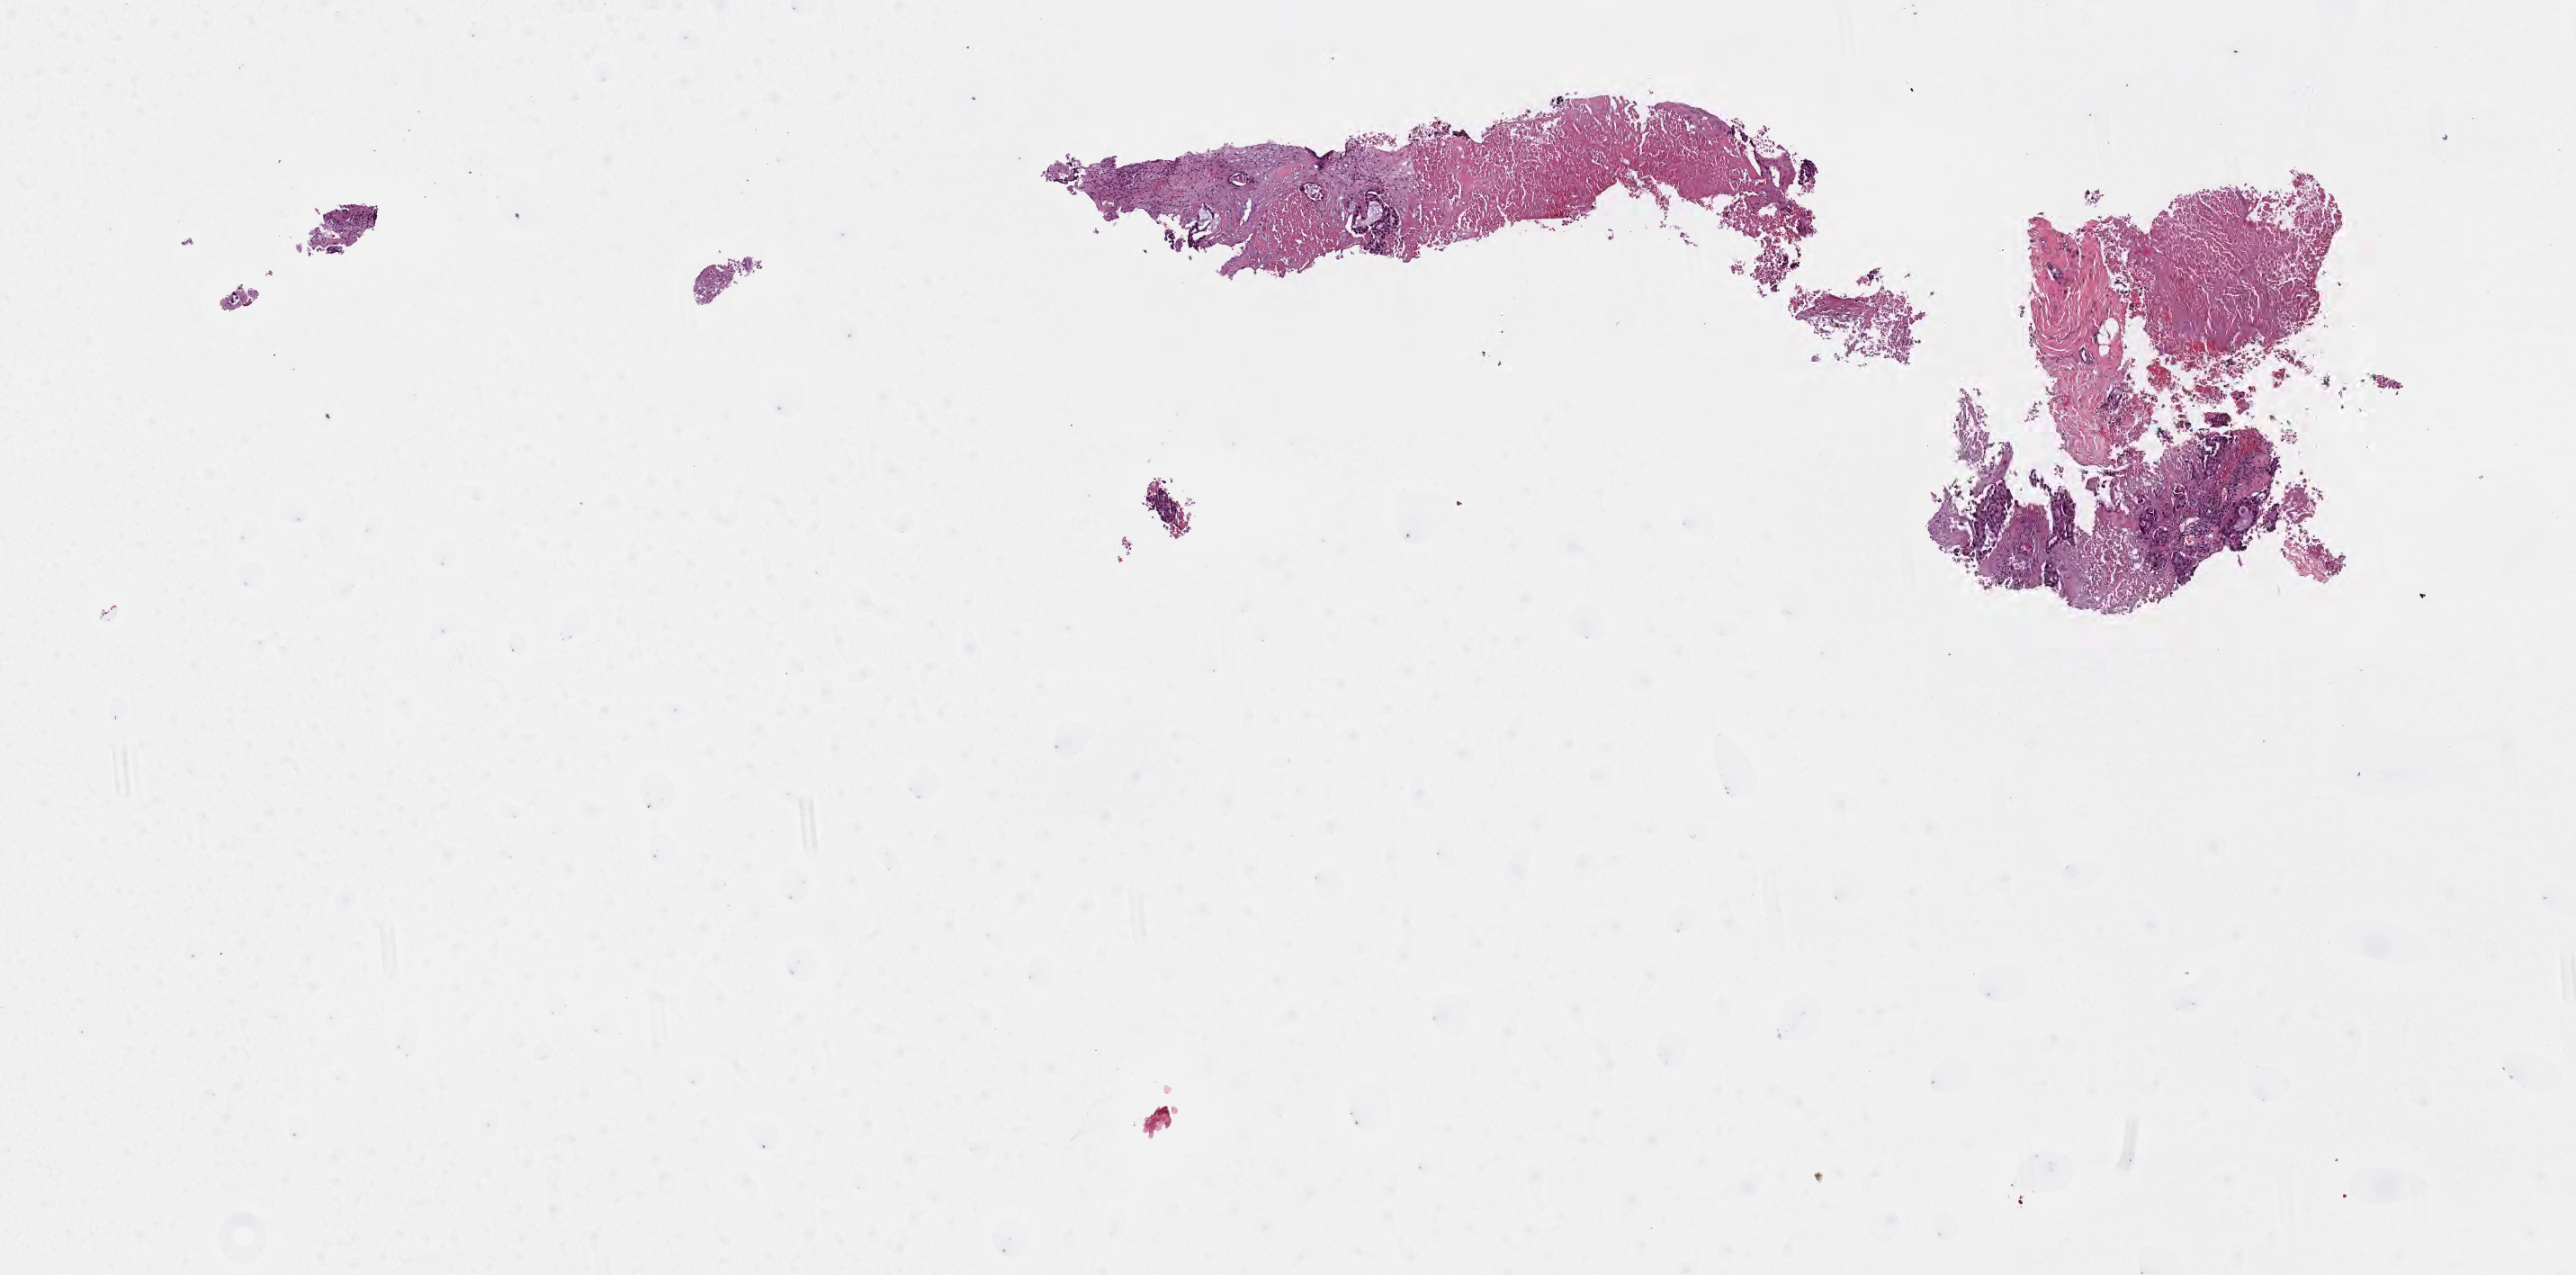
Whole-slide image, hematoxylin and eosin (H&E) stain, shown as a low-resolution overview of the whole scanned area (about 11.6 x 5.7 mm). Tumor tissue. Site: lung (right). Patient male; aged 66.
• histologic diagnosis: Adenocarcinoma, NOS